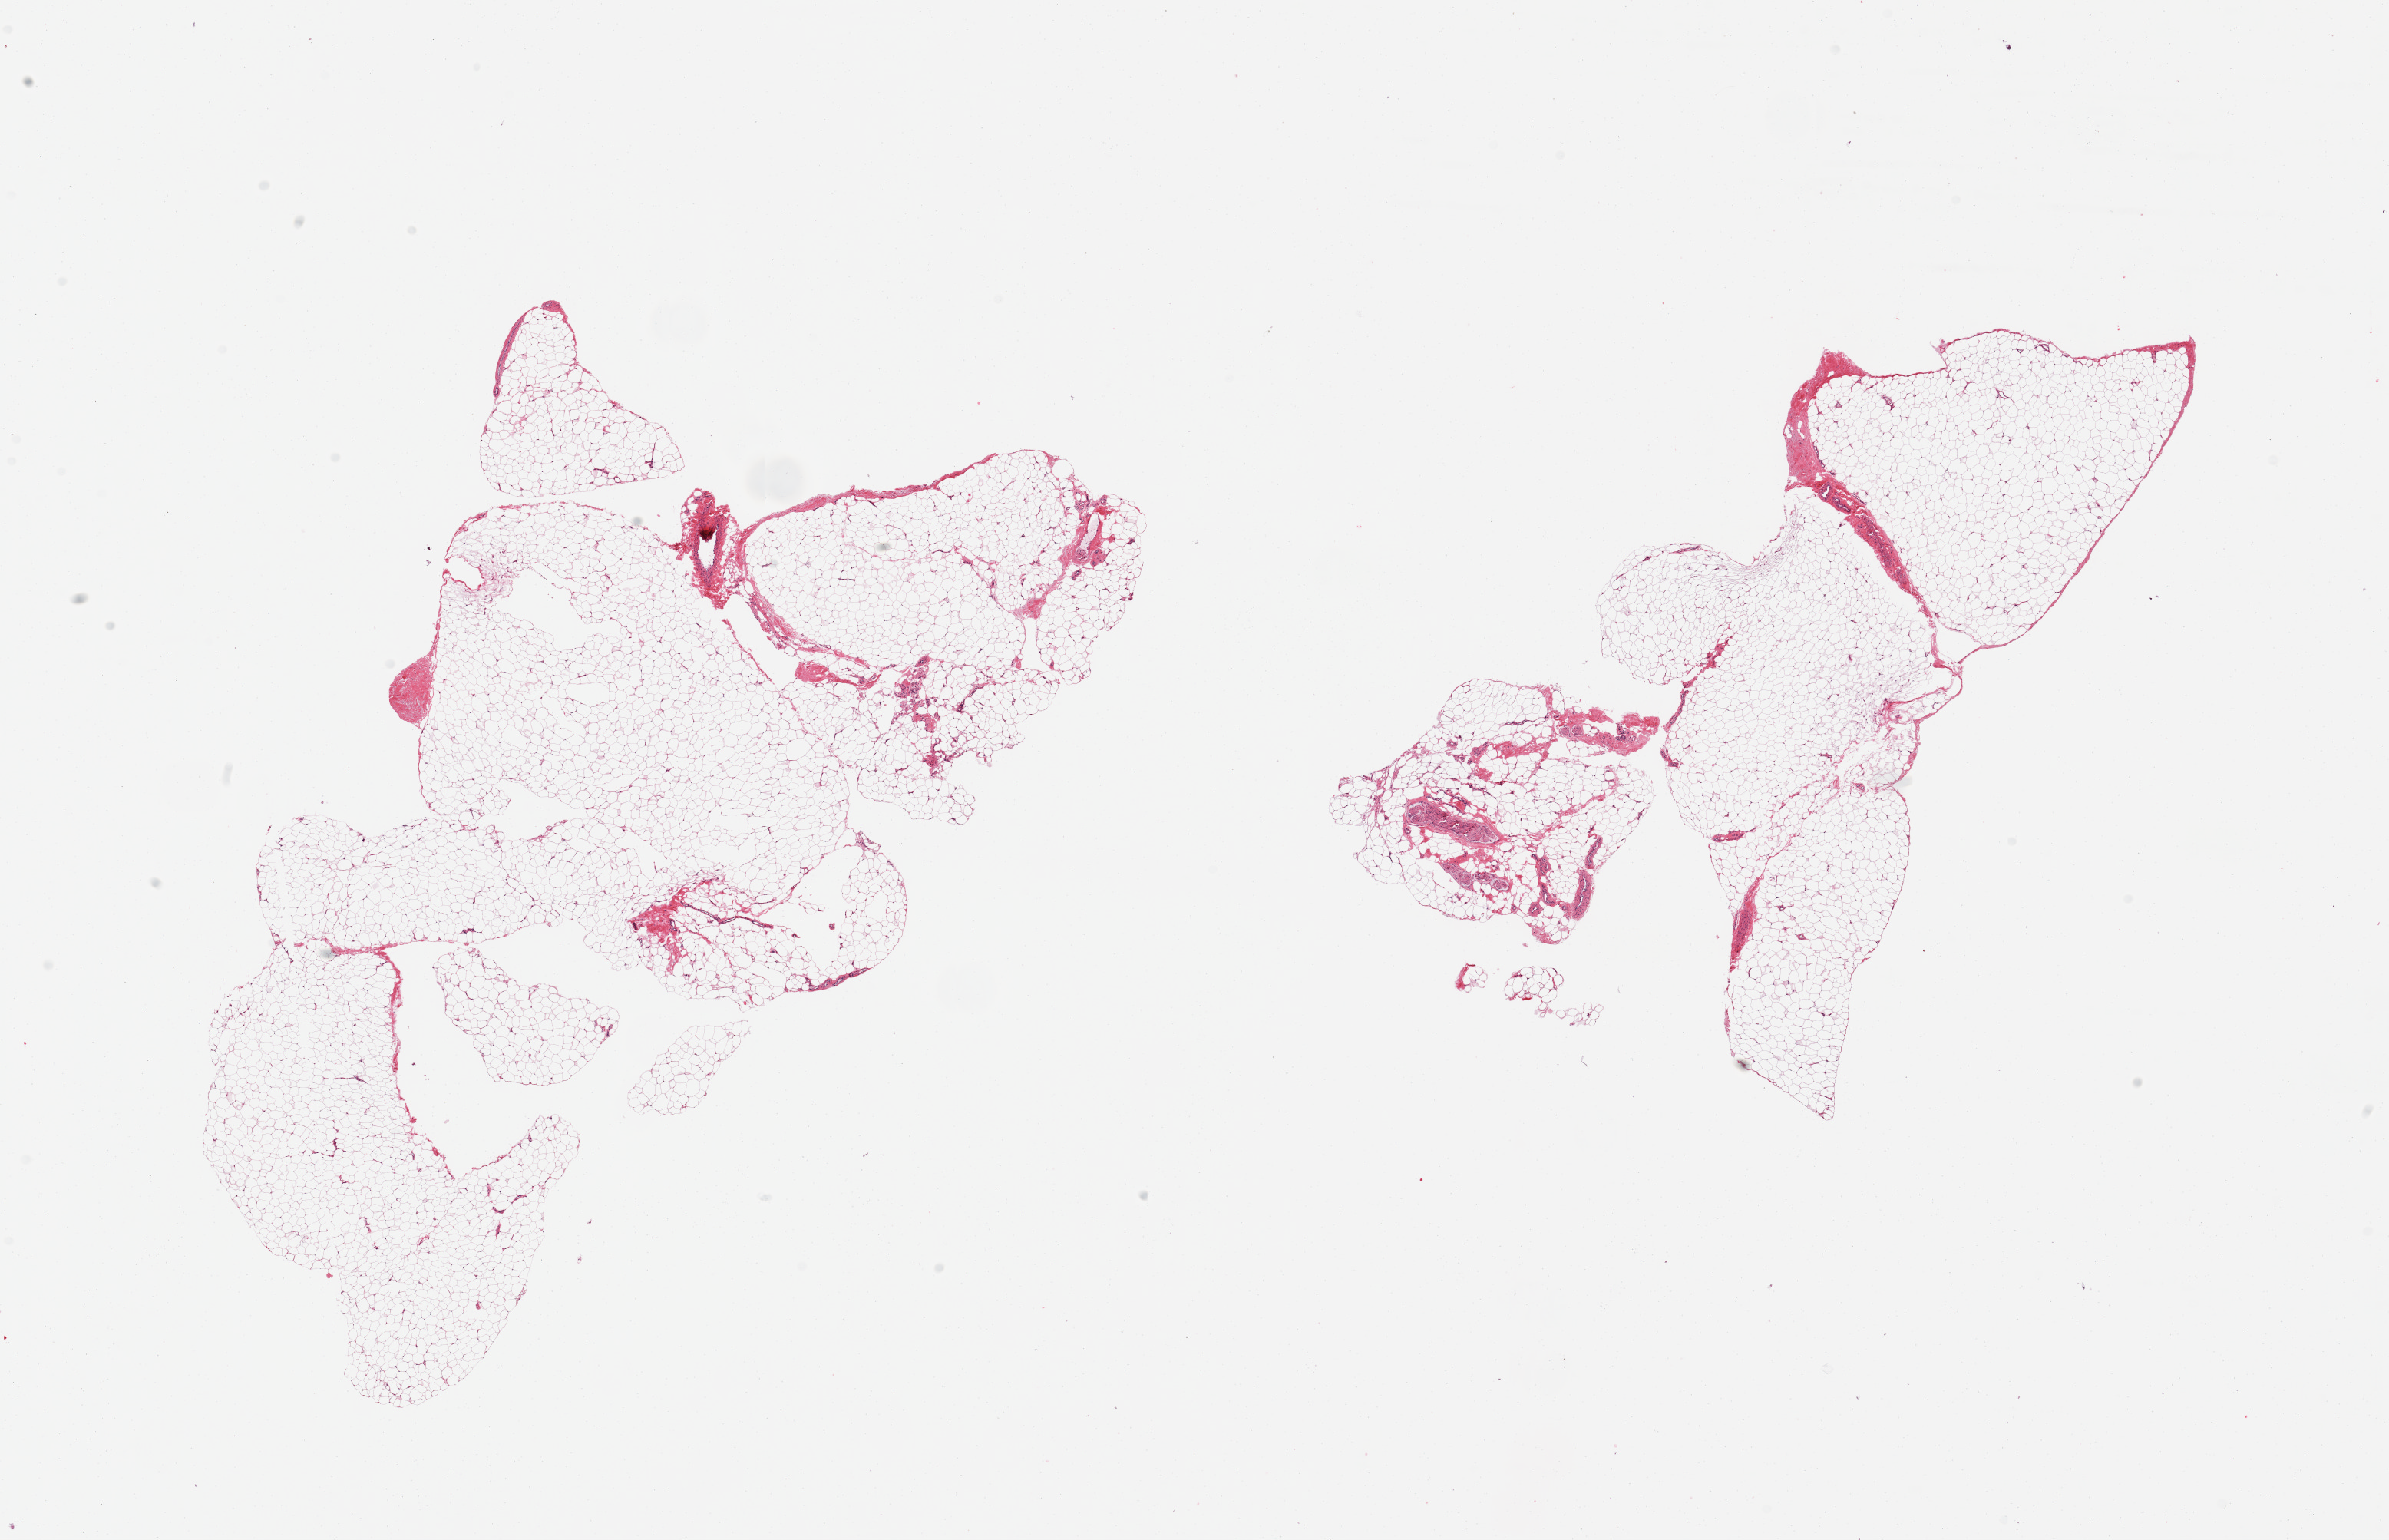
Whole-slide image, hematoxylin and eosin (H&E) stain, shown as a low-resolution overview of the whole scanned area (about 24.6 x 15.9 mm, acquisition: 20x scan). PAXgene-fixed paraffin-embedded (PFPE) section. Sampled site (target tissue): adipose tissue. Donor tissue sample. Donor: male.
* pathologist's review note for this sample: 2 pieces, ~10% fascia/peripheral nerve elements